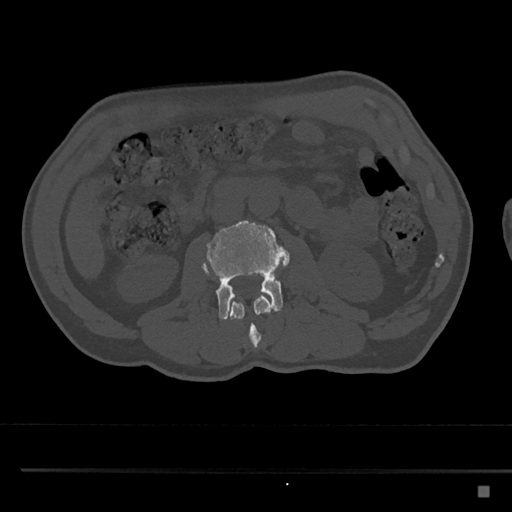
CT including the spine, one axial slice. Position 721 of 797 along the scan axis. Reconstruction kernel Br40s/3. 120 kVp. Bone window (W 1800 / L 400 HU). 0.5 mm slice thickness. 512 × 512 image matrix, field of view 391 × 391 mm. Male patient, age 59 years. Case-level facts recorded for this patient, not image findings: primary cancer: prostate.
Annotated regions visible in this slice (semi-automatically segmented with operator editing):
- L2 vertebra: bounding box [x1, y1, x2, y2] px = [204, 266, 272, 348]
- L3 vertebra: [201, 221, 290, 320]